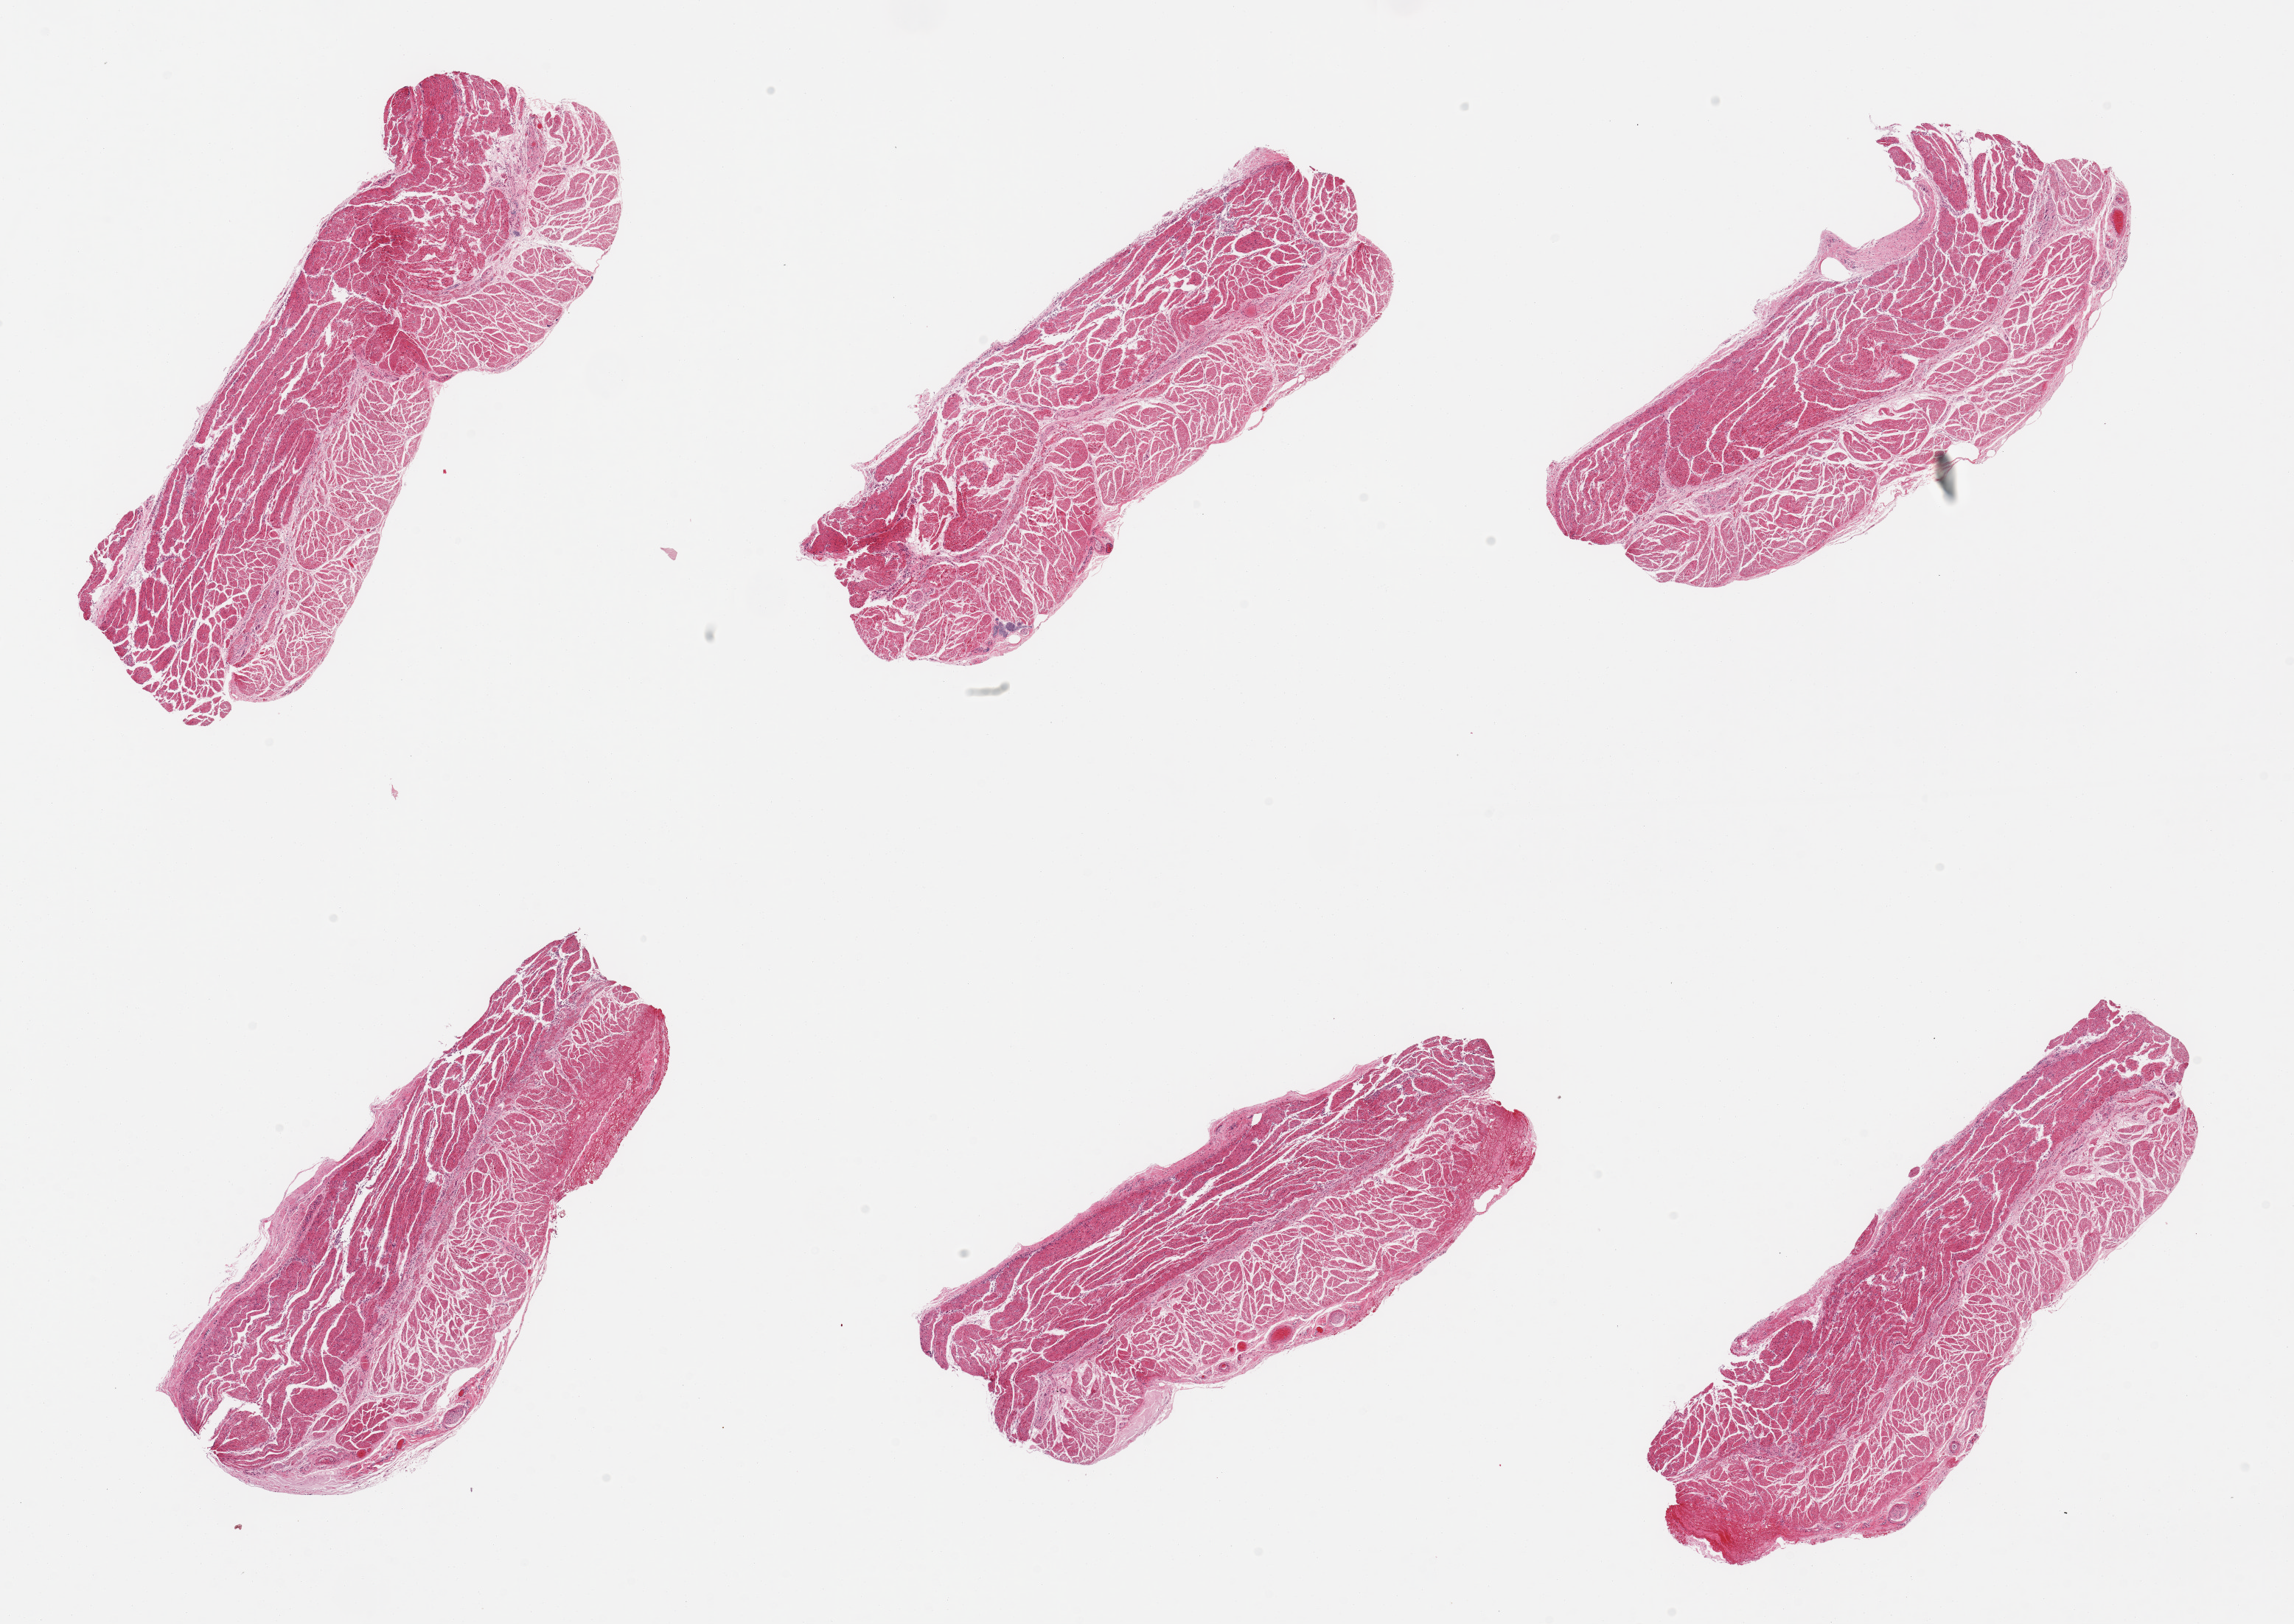
Whole-slide image, hematoxylin and eosin (H&E) stain — whole scanned area (about 24.6 x 17.4 mm) shown as a low-resolution overview; PAXgene-fixed, paraffin-embedded tissue; section of esophageal muscle (target tissue); tissue donor sample. Female donor.
Review note (as recorded): 6 pieces, all target muscualaris.